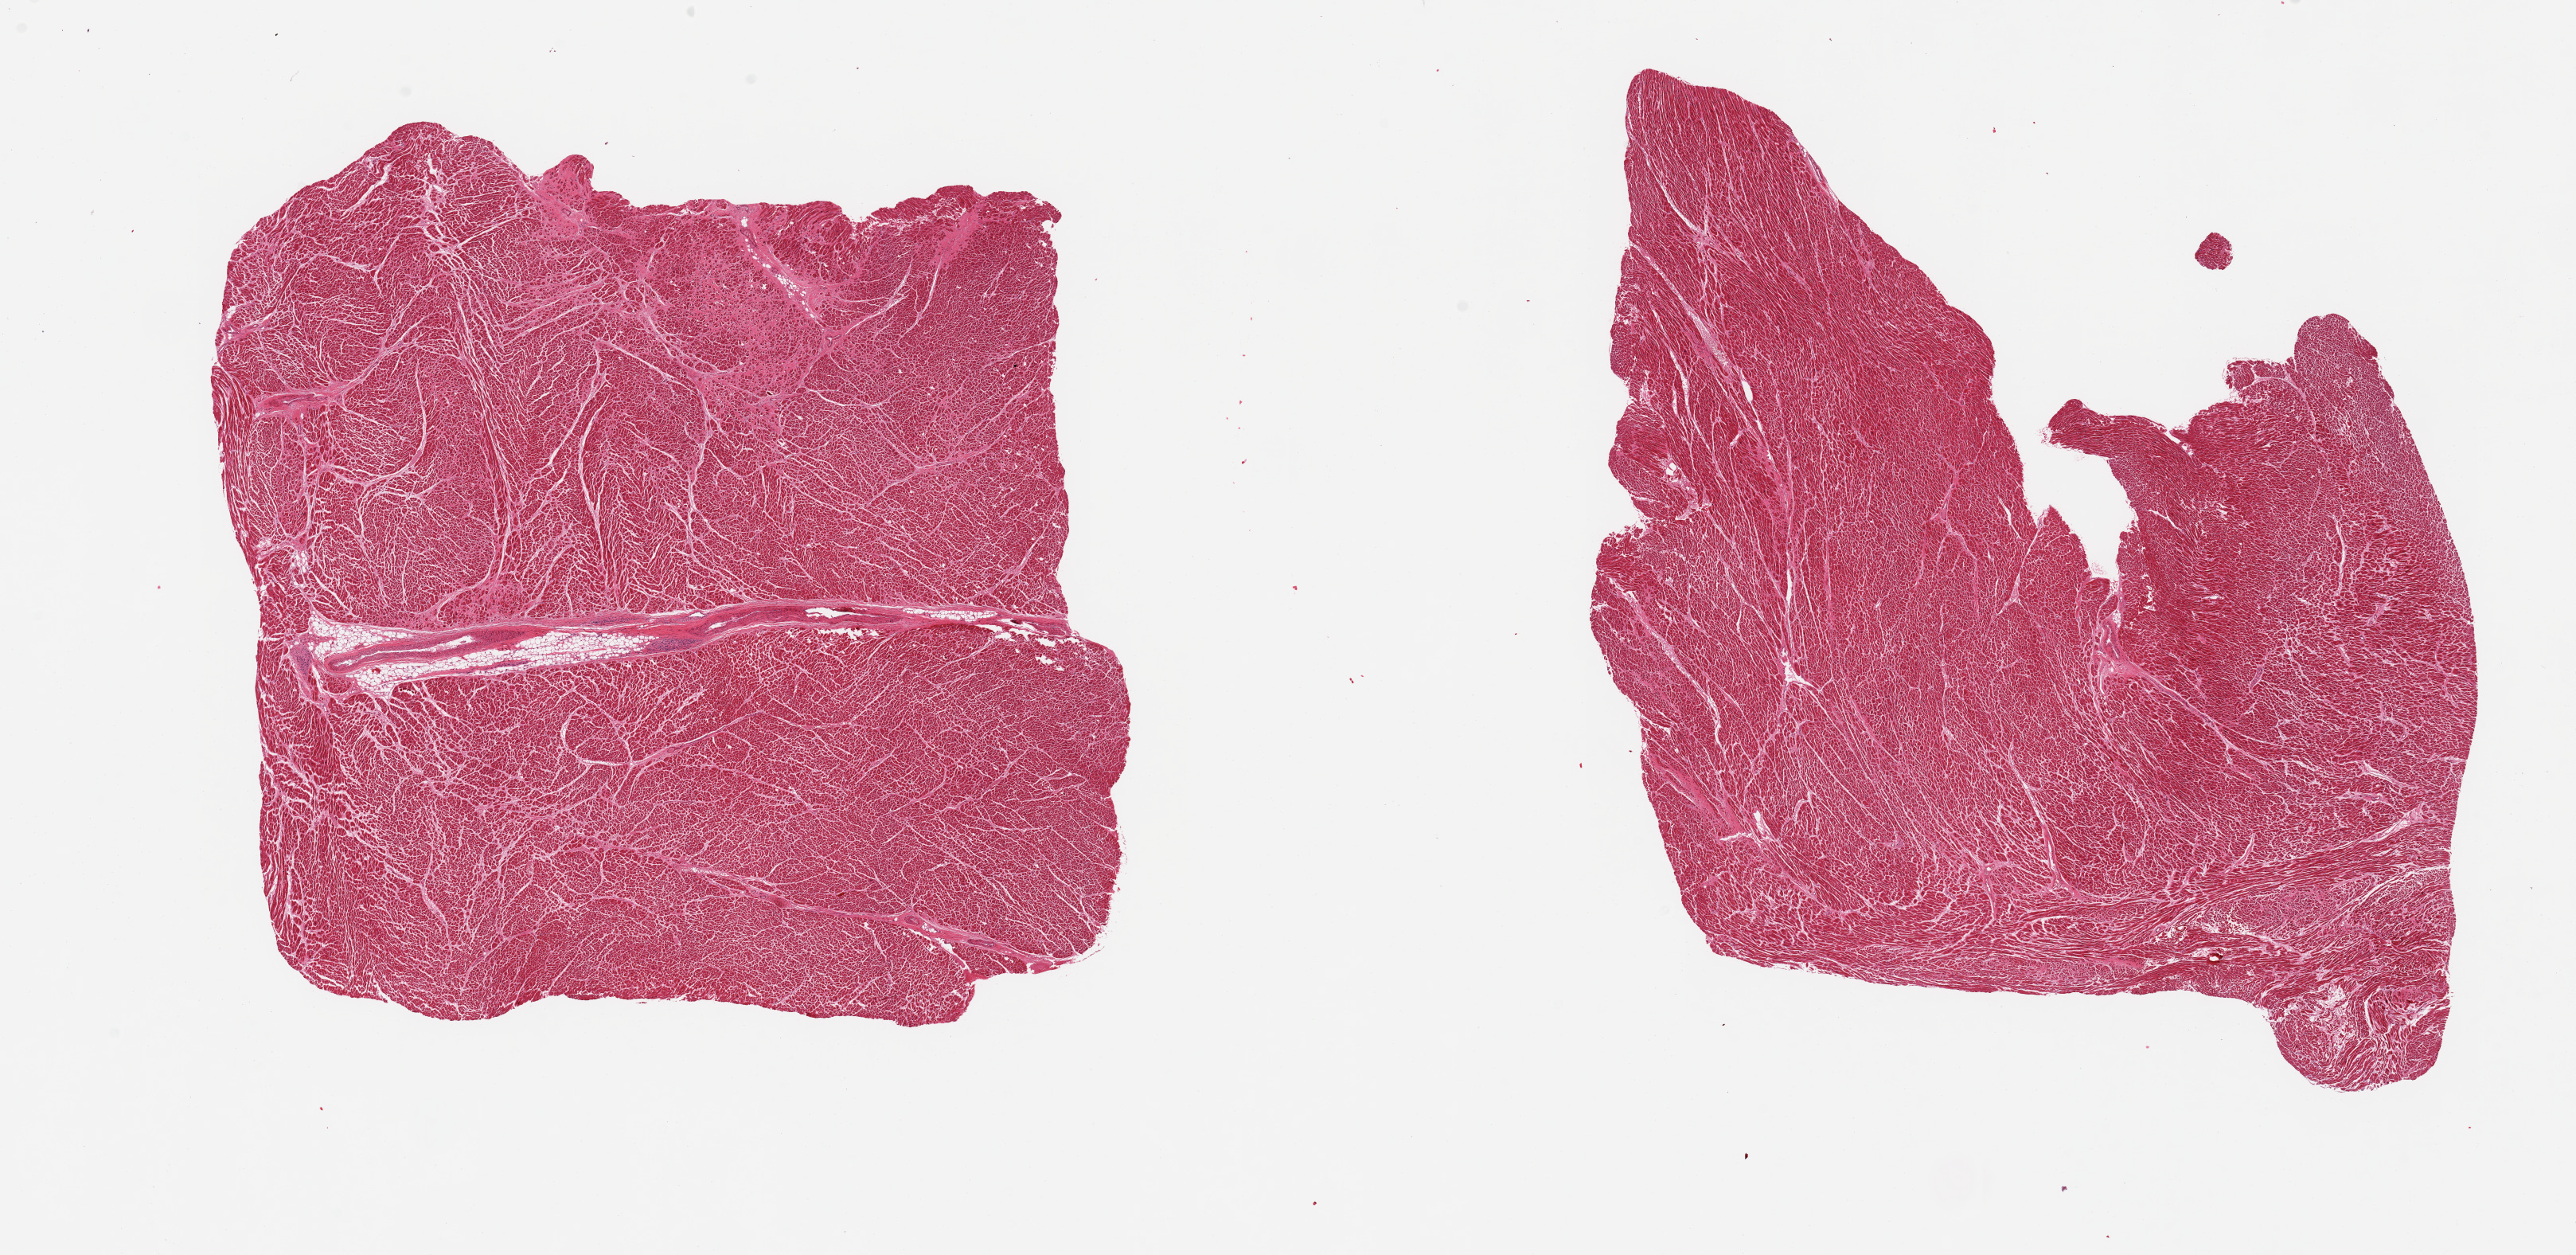
Whole-slide image, haematoxylin and eosin stain — a low-resolution overview of the entire scanned area, about 25.6 x 12.5 mm; PAXgene-fixed, paraffin-embedded tissue; section of heart (target tissue); tissue donor sample. Donor: male.
Review note (as recorded): 2 pieces; one piece with focus of interstitial fibrosis and scarring, myocyte hypertrophy.